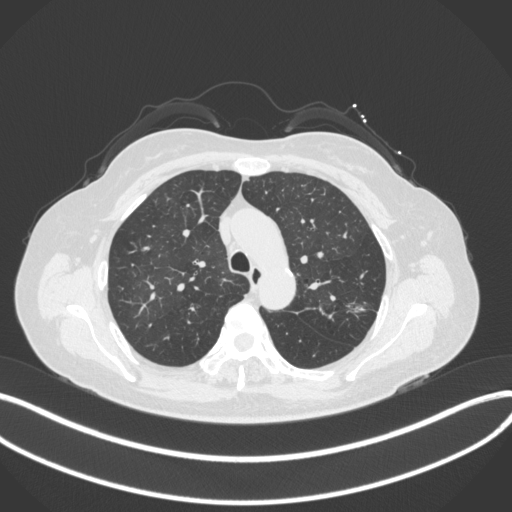
Chest CT, one axial slice; slice 252 of 330 in the series (ordered by position); 120 kVp; lung window (W 1500 / L -600 HU); 1 mm slice thickness; 512 × 512 image matrix, field of view 400 × 400 mm. Patient: female, 60 years. From the clinical record (not read from this slice): clinical TNM (as recorded): T1c N0 M0.
Outlined on this slice (rectangle marked by the reading radiologist):
- lung tumour (recorded histology: adenocarcinoma): bounding box (x1, y1, x2, y2) in pixels: (345, 295, 365, 321)